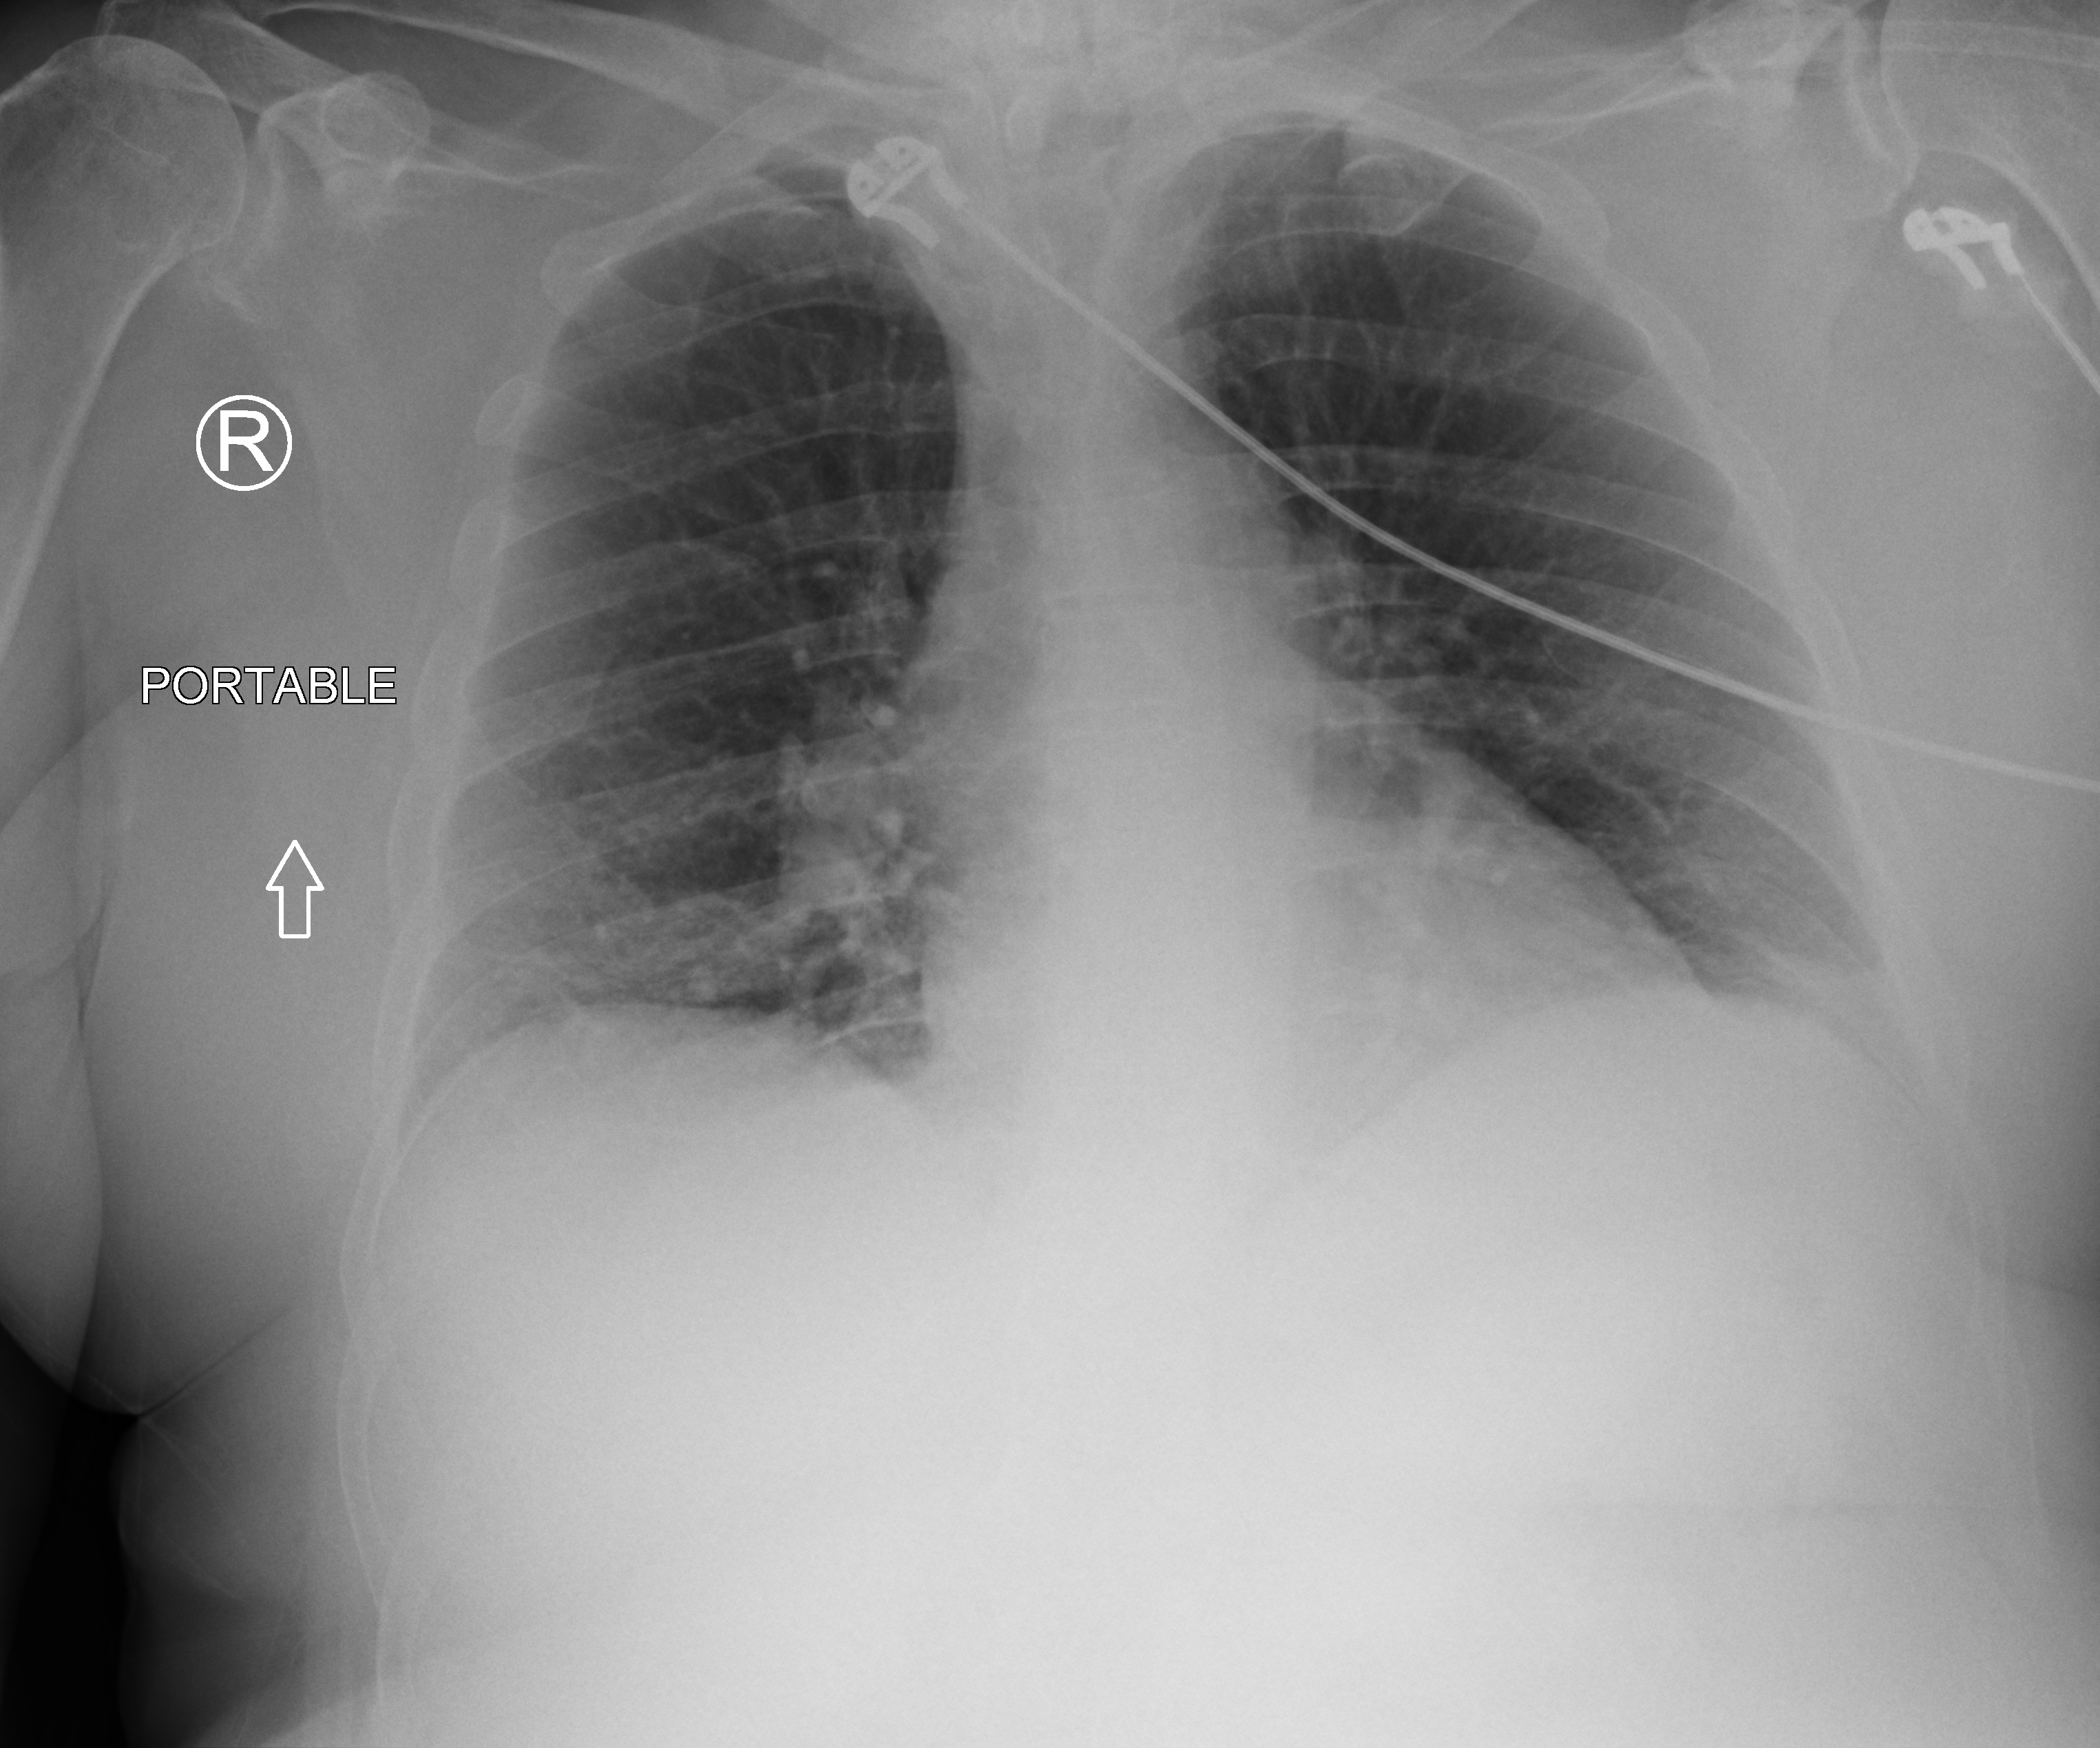
Bedside chest radiograph (computed radiography). Patient hospitalised with COVID-19; male, aged 60–74 years.
Admission-level facts for this patient (not findings on this image; timing relative to this image not recorded): mechanically ventilated during this hospital stay: no; length of hospital stay: 30 days.